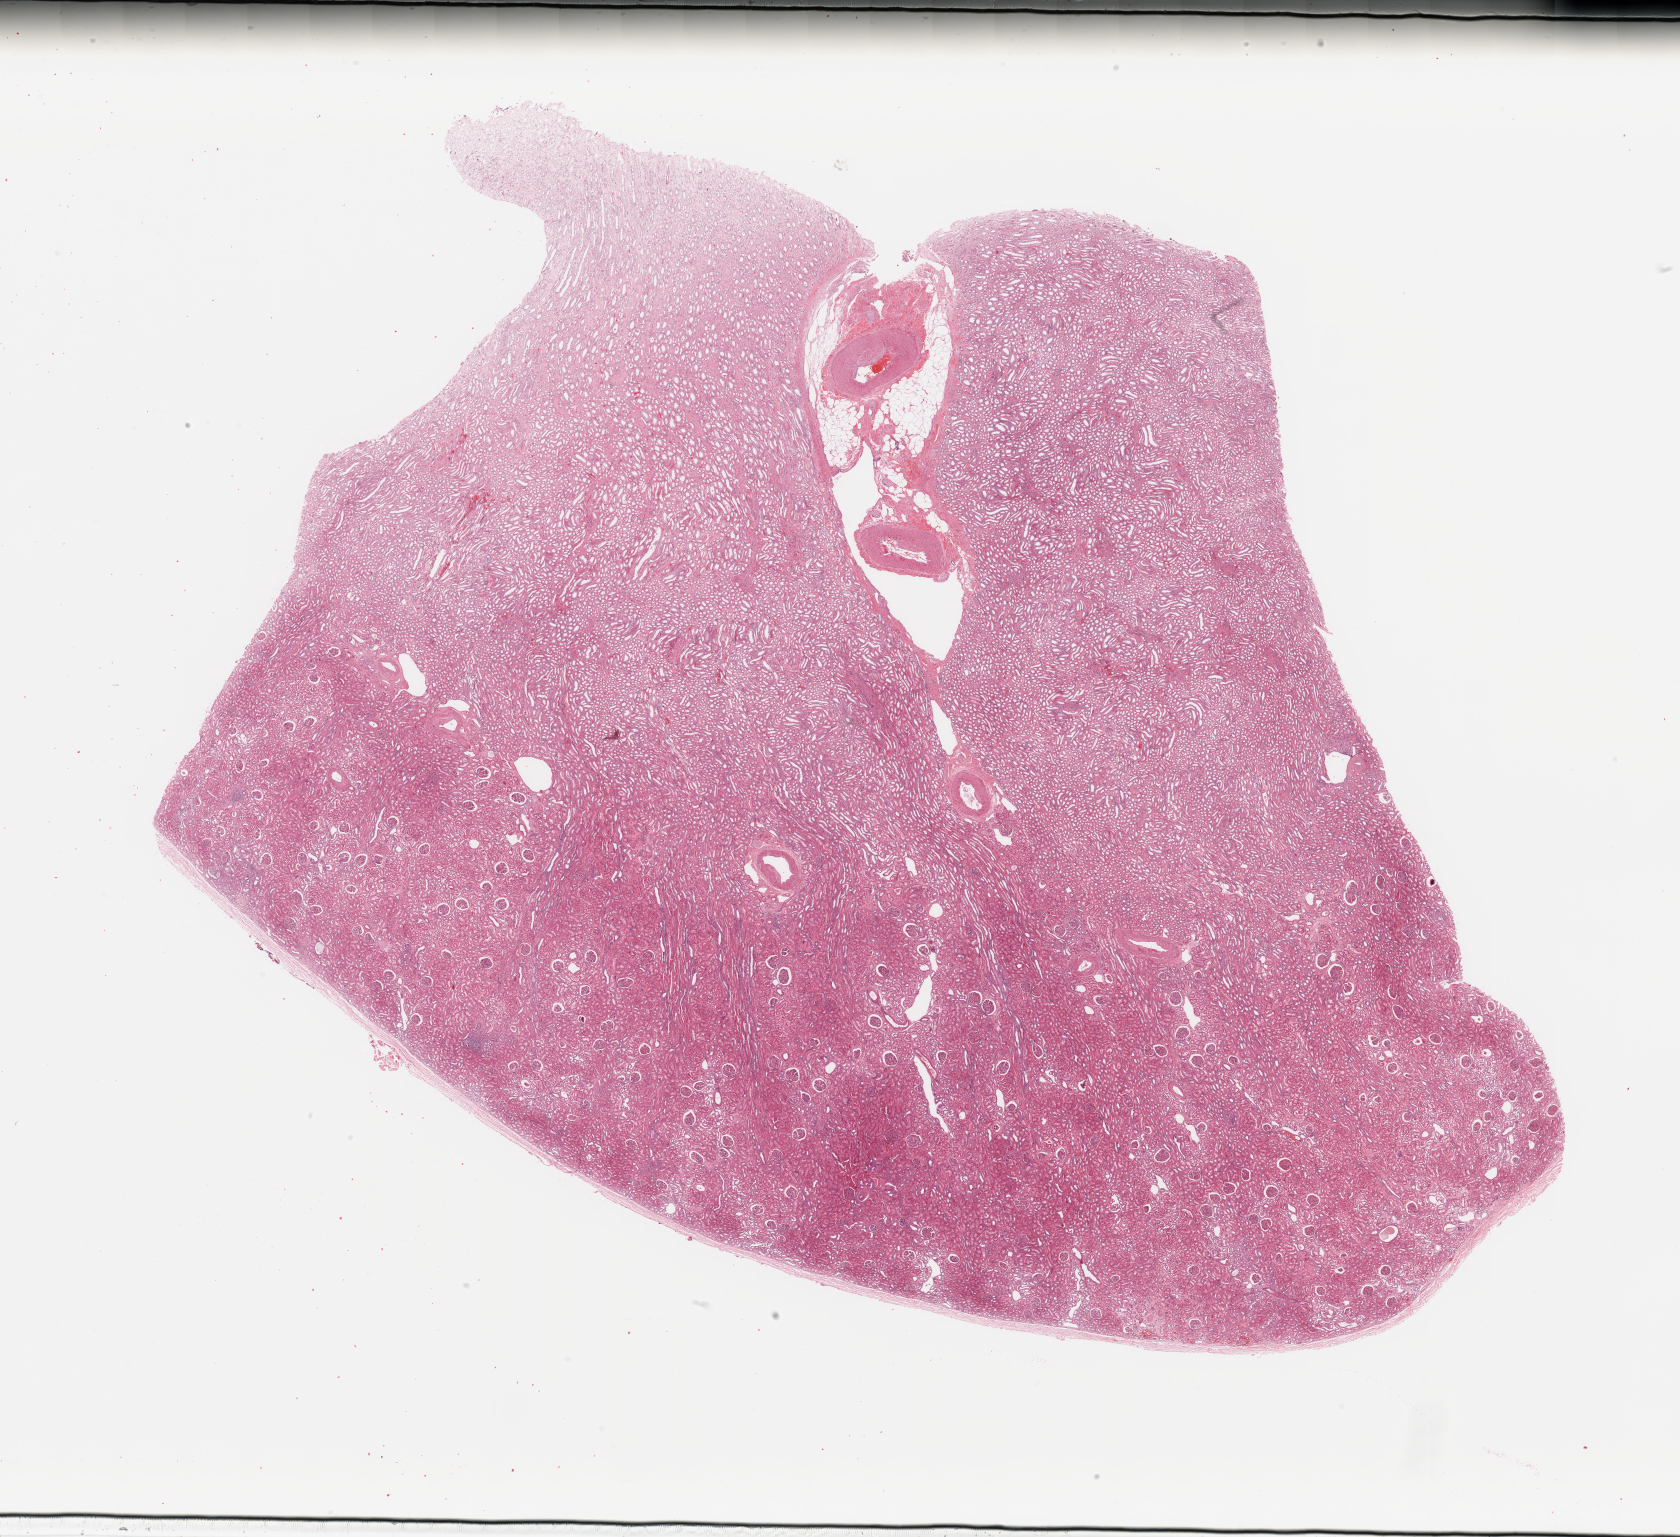
Digitized Hematoxylin and eosin (H&E) stained tissue section (whole slide), a low-resolution overview of the entire scanned area, about 26.6 x 24.3 mm (slide scanned at 20x). Normal (non-tumour) tissue sample, kidney. Patient: female, age 57 years.
This section: normal (non-tumour) tissue from the same patient. Patient diagnosis: Renal cell carcinoma, NOS.